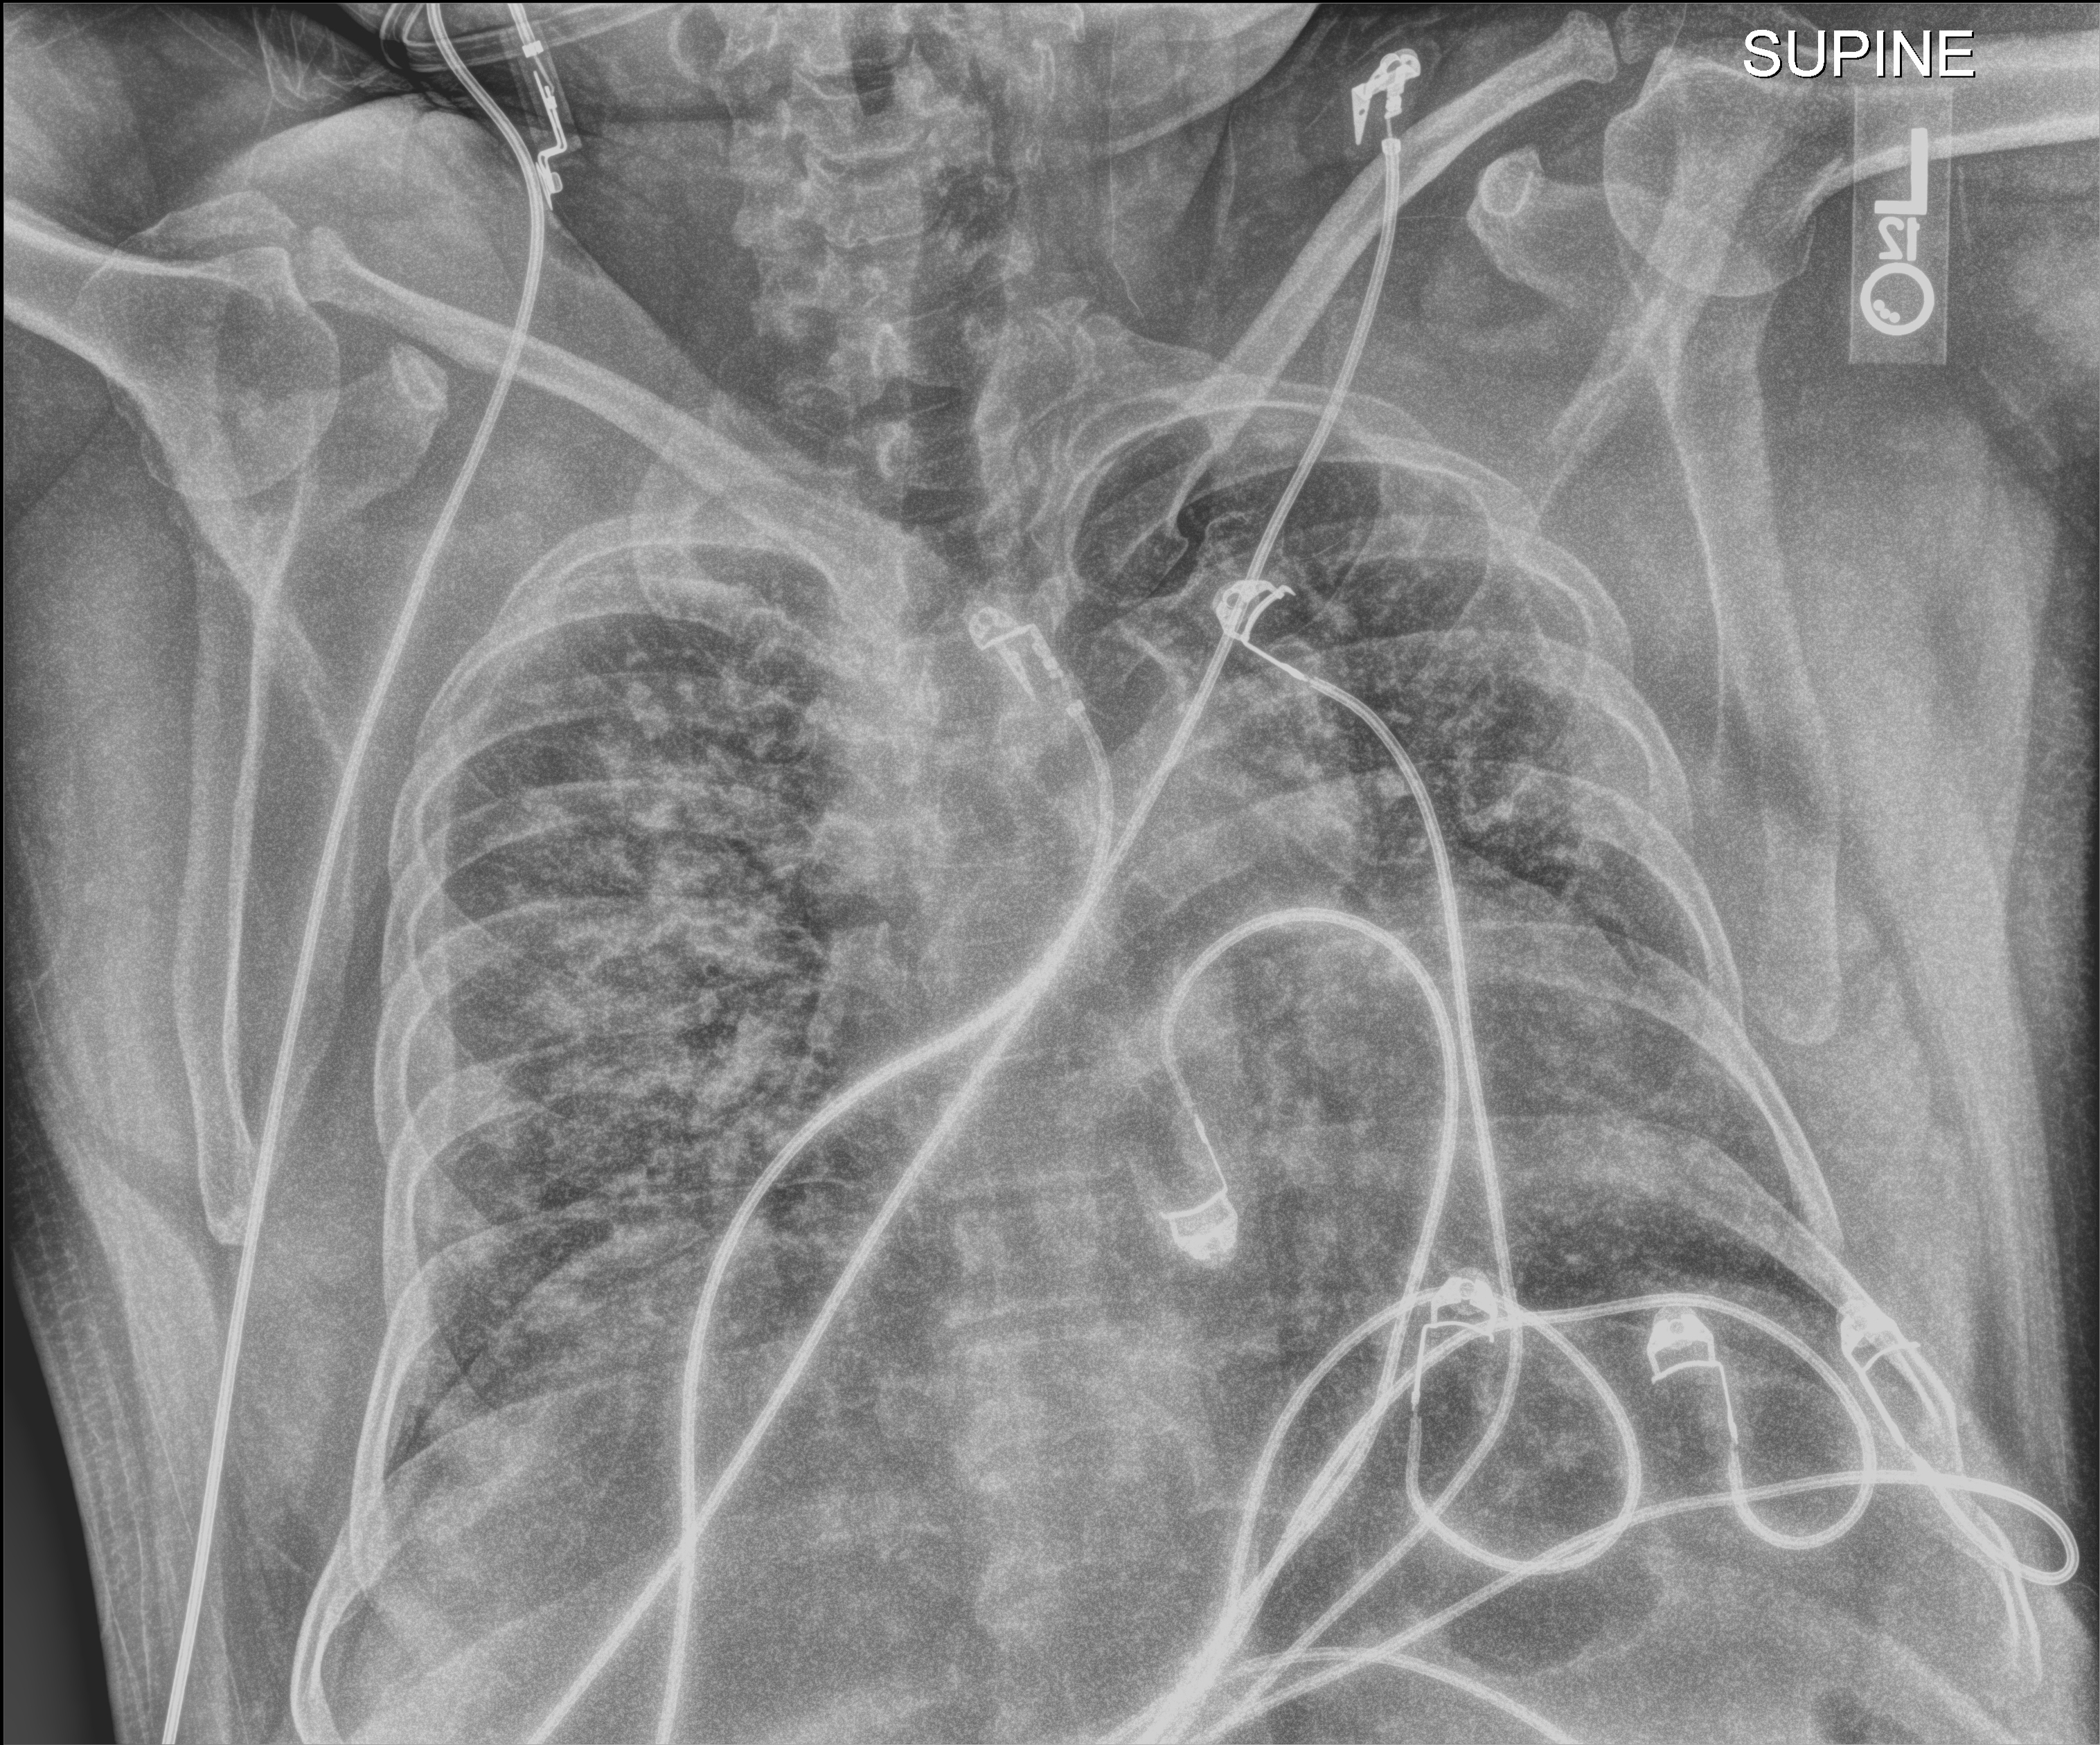
Chest X-ray; anteroposterior (AP) projection. Patient hospitalised with COVID-19, aged 18–59 years.
Hospital-stay facts (about this admission, not read from this image; timing relative to this image not recorded): mechanically ventilated during this hospital stay: yes.